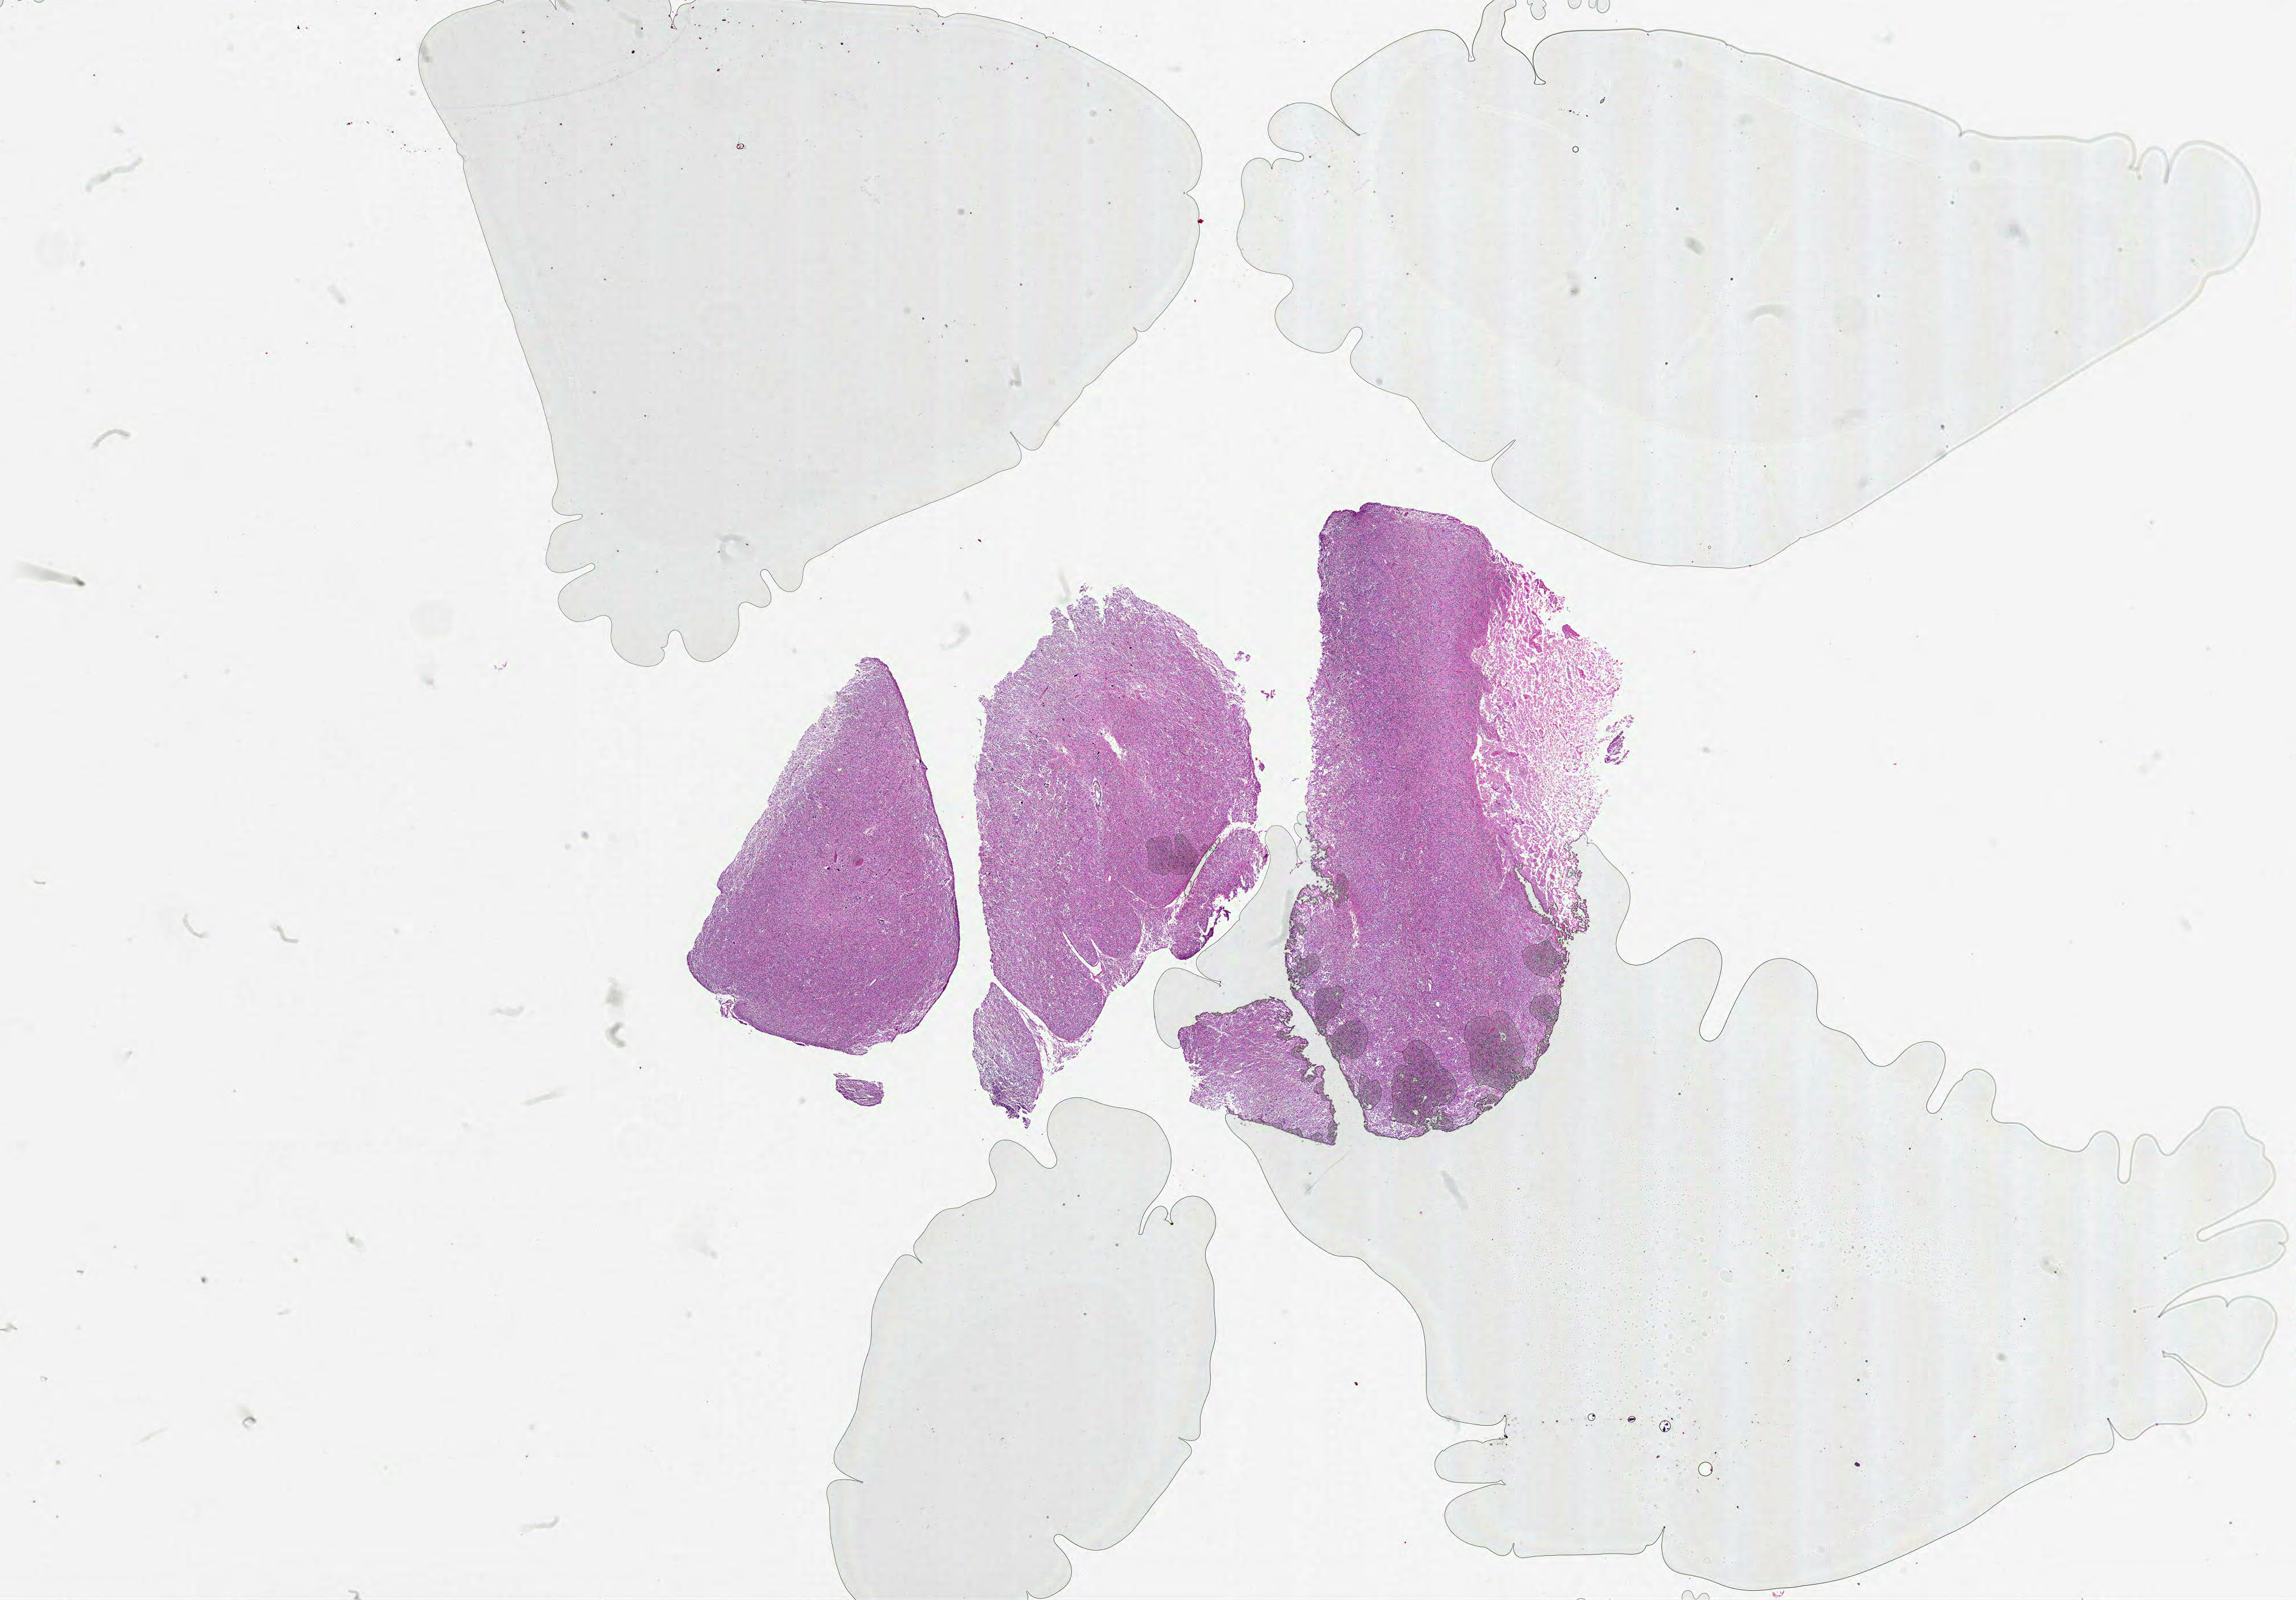
Whole-slide histology image, Hematoxylin and eosin (H&E) stained, shown as a low-resolution overview of the whole scanned area (about 32.0 x 22.3 mm, slide scanned at 20x), formalin-fixed paraffin-embedded (FFPE) diagnostic section, sample: primary tumour, brain. Male patient; age at initial diagnosis 52 years.
Pathologic diagnosis: Glioblastoma.